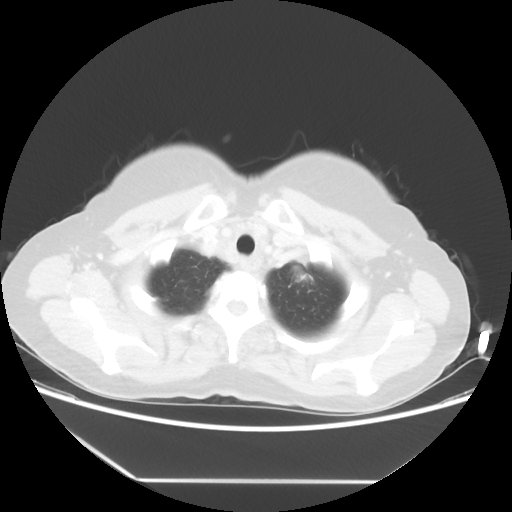
Chest CT, one axial slice. Slice 47 of 52 in the series (ordered by position). Reconstruction kernel STANDARD. Lung window (W 1500 / L -600 HU). 512 × 512 image matrix, field of view 390 × 390 mm. Female patient, age 50 years. Case-level facts recorded for this patient, not image findings: clinical TNM (as recorded): T2 N3 M0.
Outlined on this slice (bounding box drawn by a radiologist):
- lung tumour (recorded histology: adenocarcinoma): bounding box <283,259,323,300> (left, top, right, bottom; pixels)